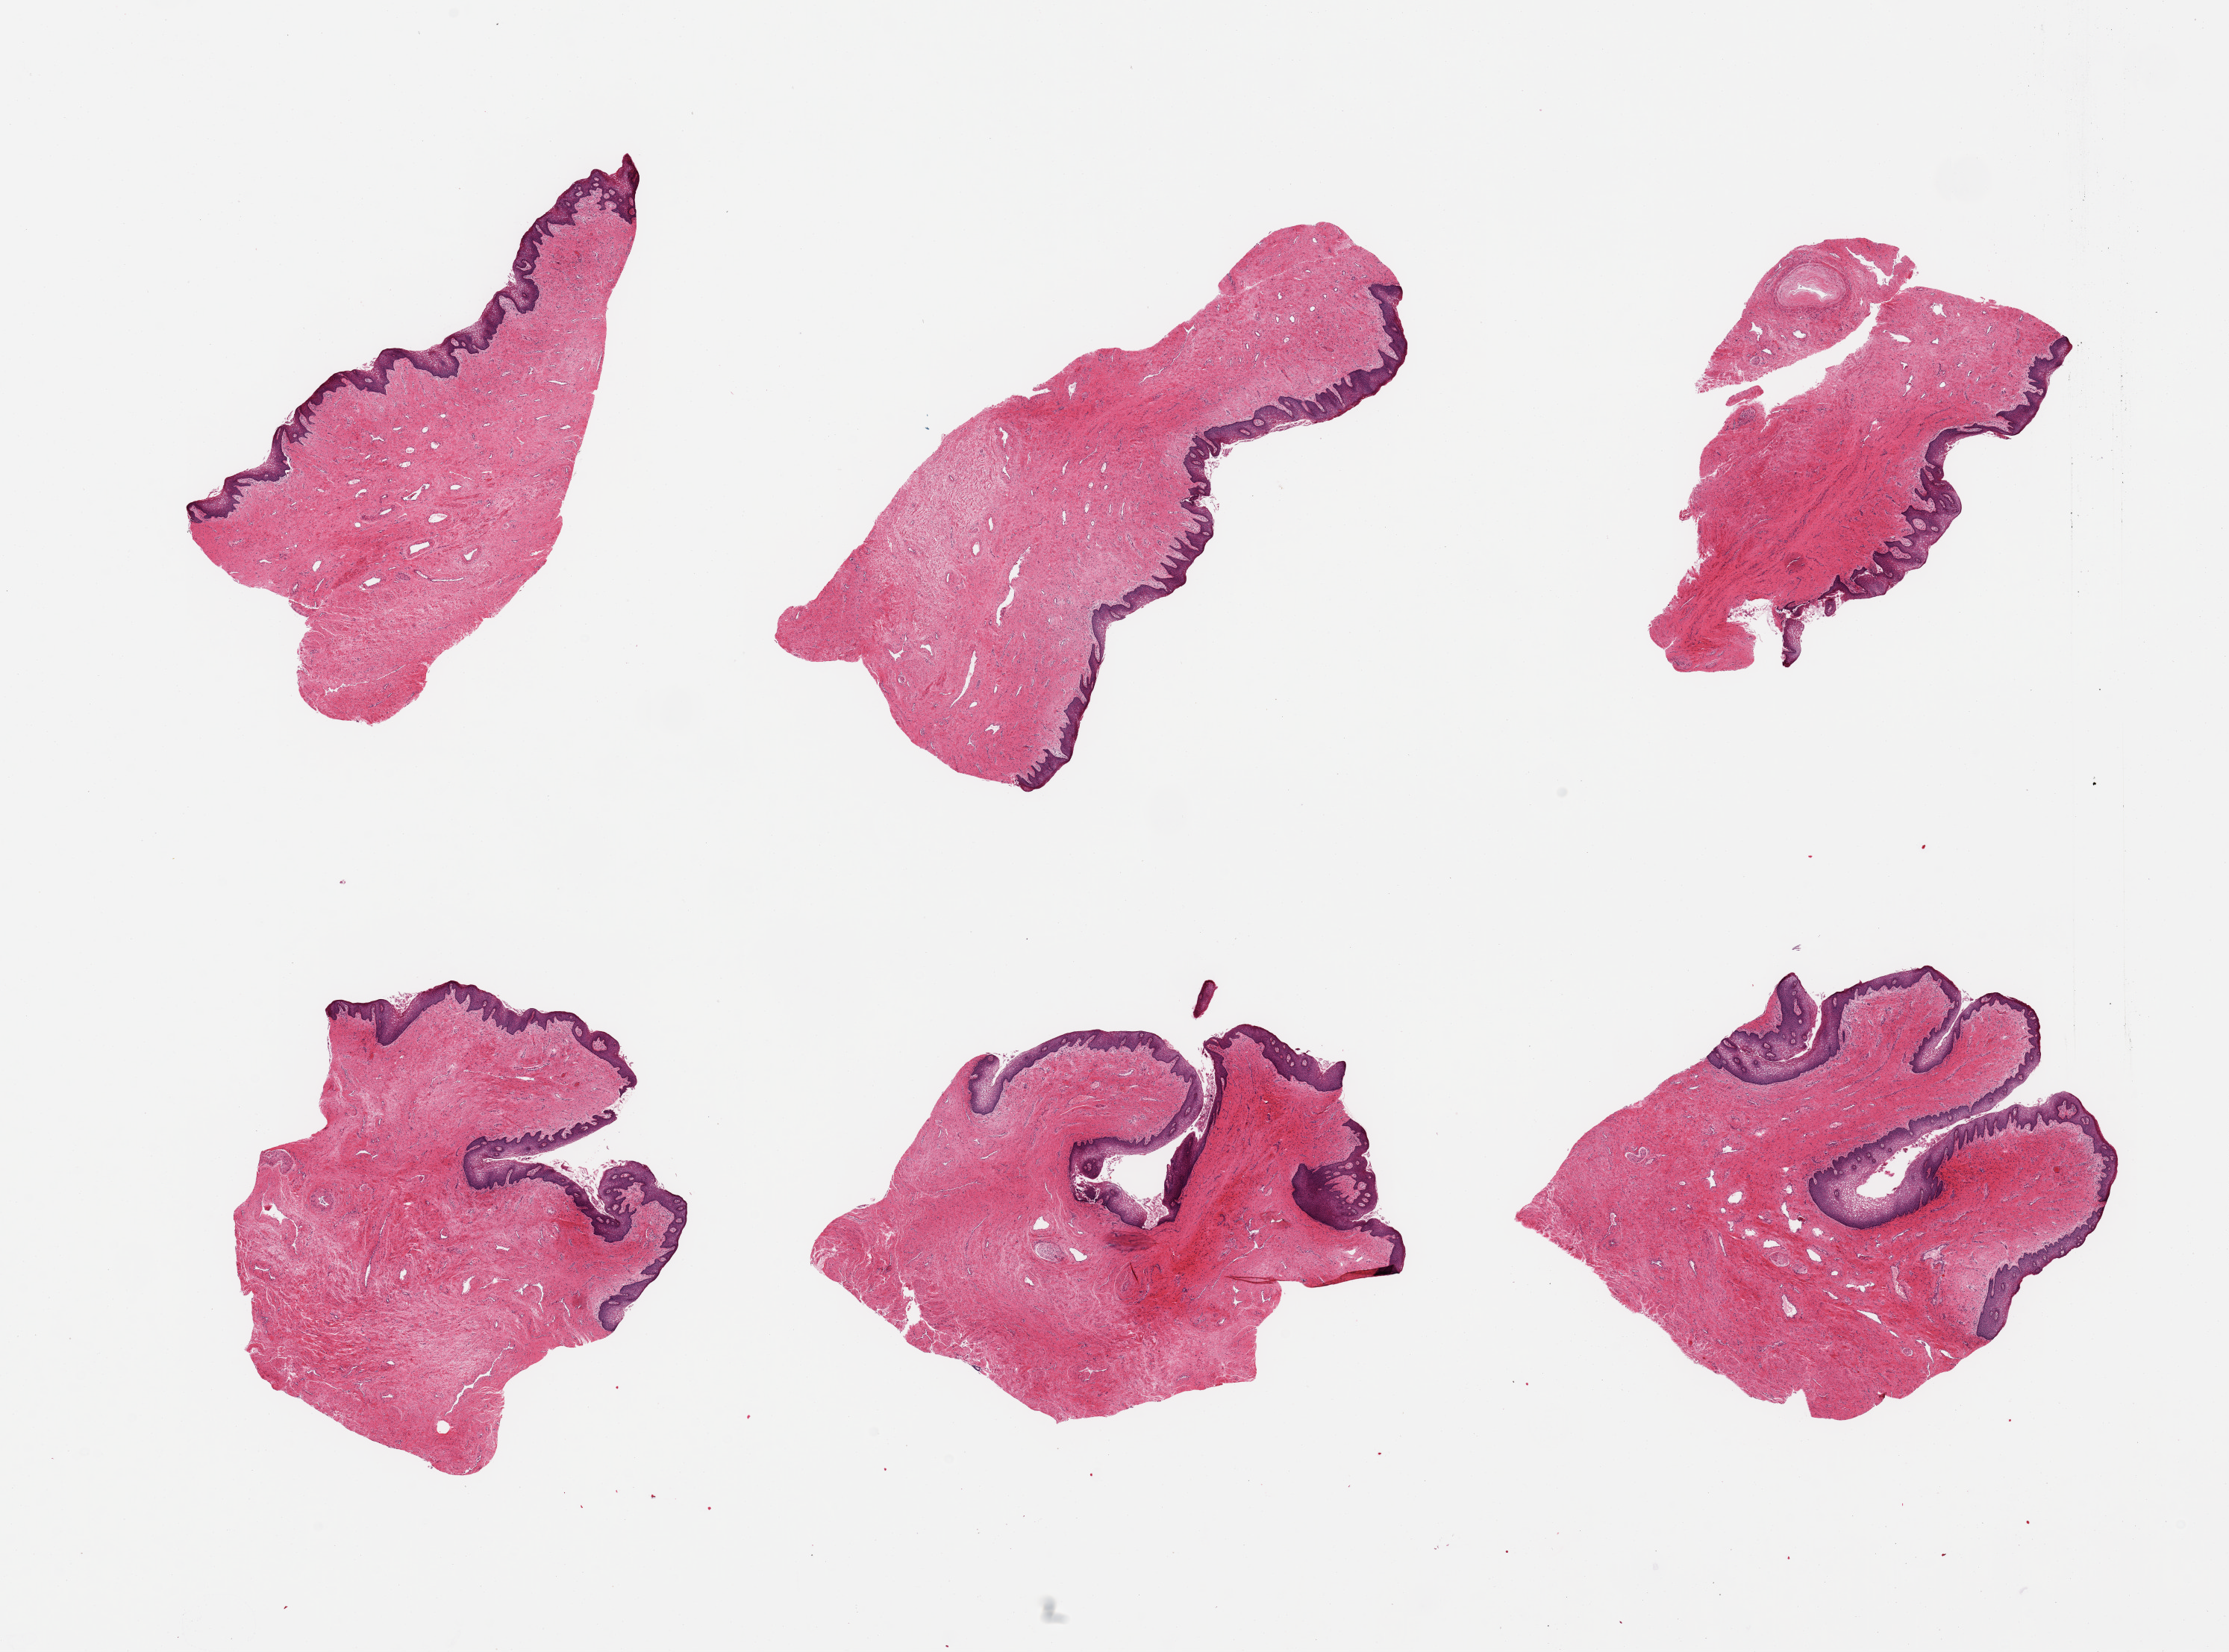
Whole-slide image, hematoxylin and eosin (H&E) stain, whole scanned area (about 23.6 x 17.5 mm) shown as a low-resolution overview, PAXgene-fixed, paraffin-embedded tissue, sampled site (target tissue): vagina, tissue donor sample. Donor sex: female.
Pathologist's review note for this sample: 6 pieces.